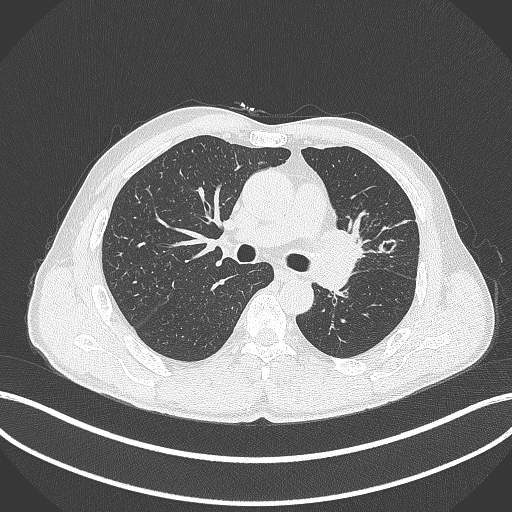
Chest CT, one axial slice; position 256 of 429 along the scan axis; 120 kVp; lung window (W 1500 / L -600 HU); 512 × 512 image matrix, field of view 400 × 400 mm. Male patient, age 57 years. From the clinical record (not read from this slice): clinical TNM (as recorded): T2b N0 M0.
Annotated regions visible in this slice (bounding box drawn by a radiologist):
- lung tumour (recorded histology: squamous cell carcinoma): bounding box (x1, y1, x2, y2) in pixels: (321, 226, 372, 263)